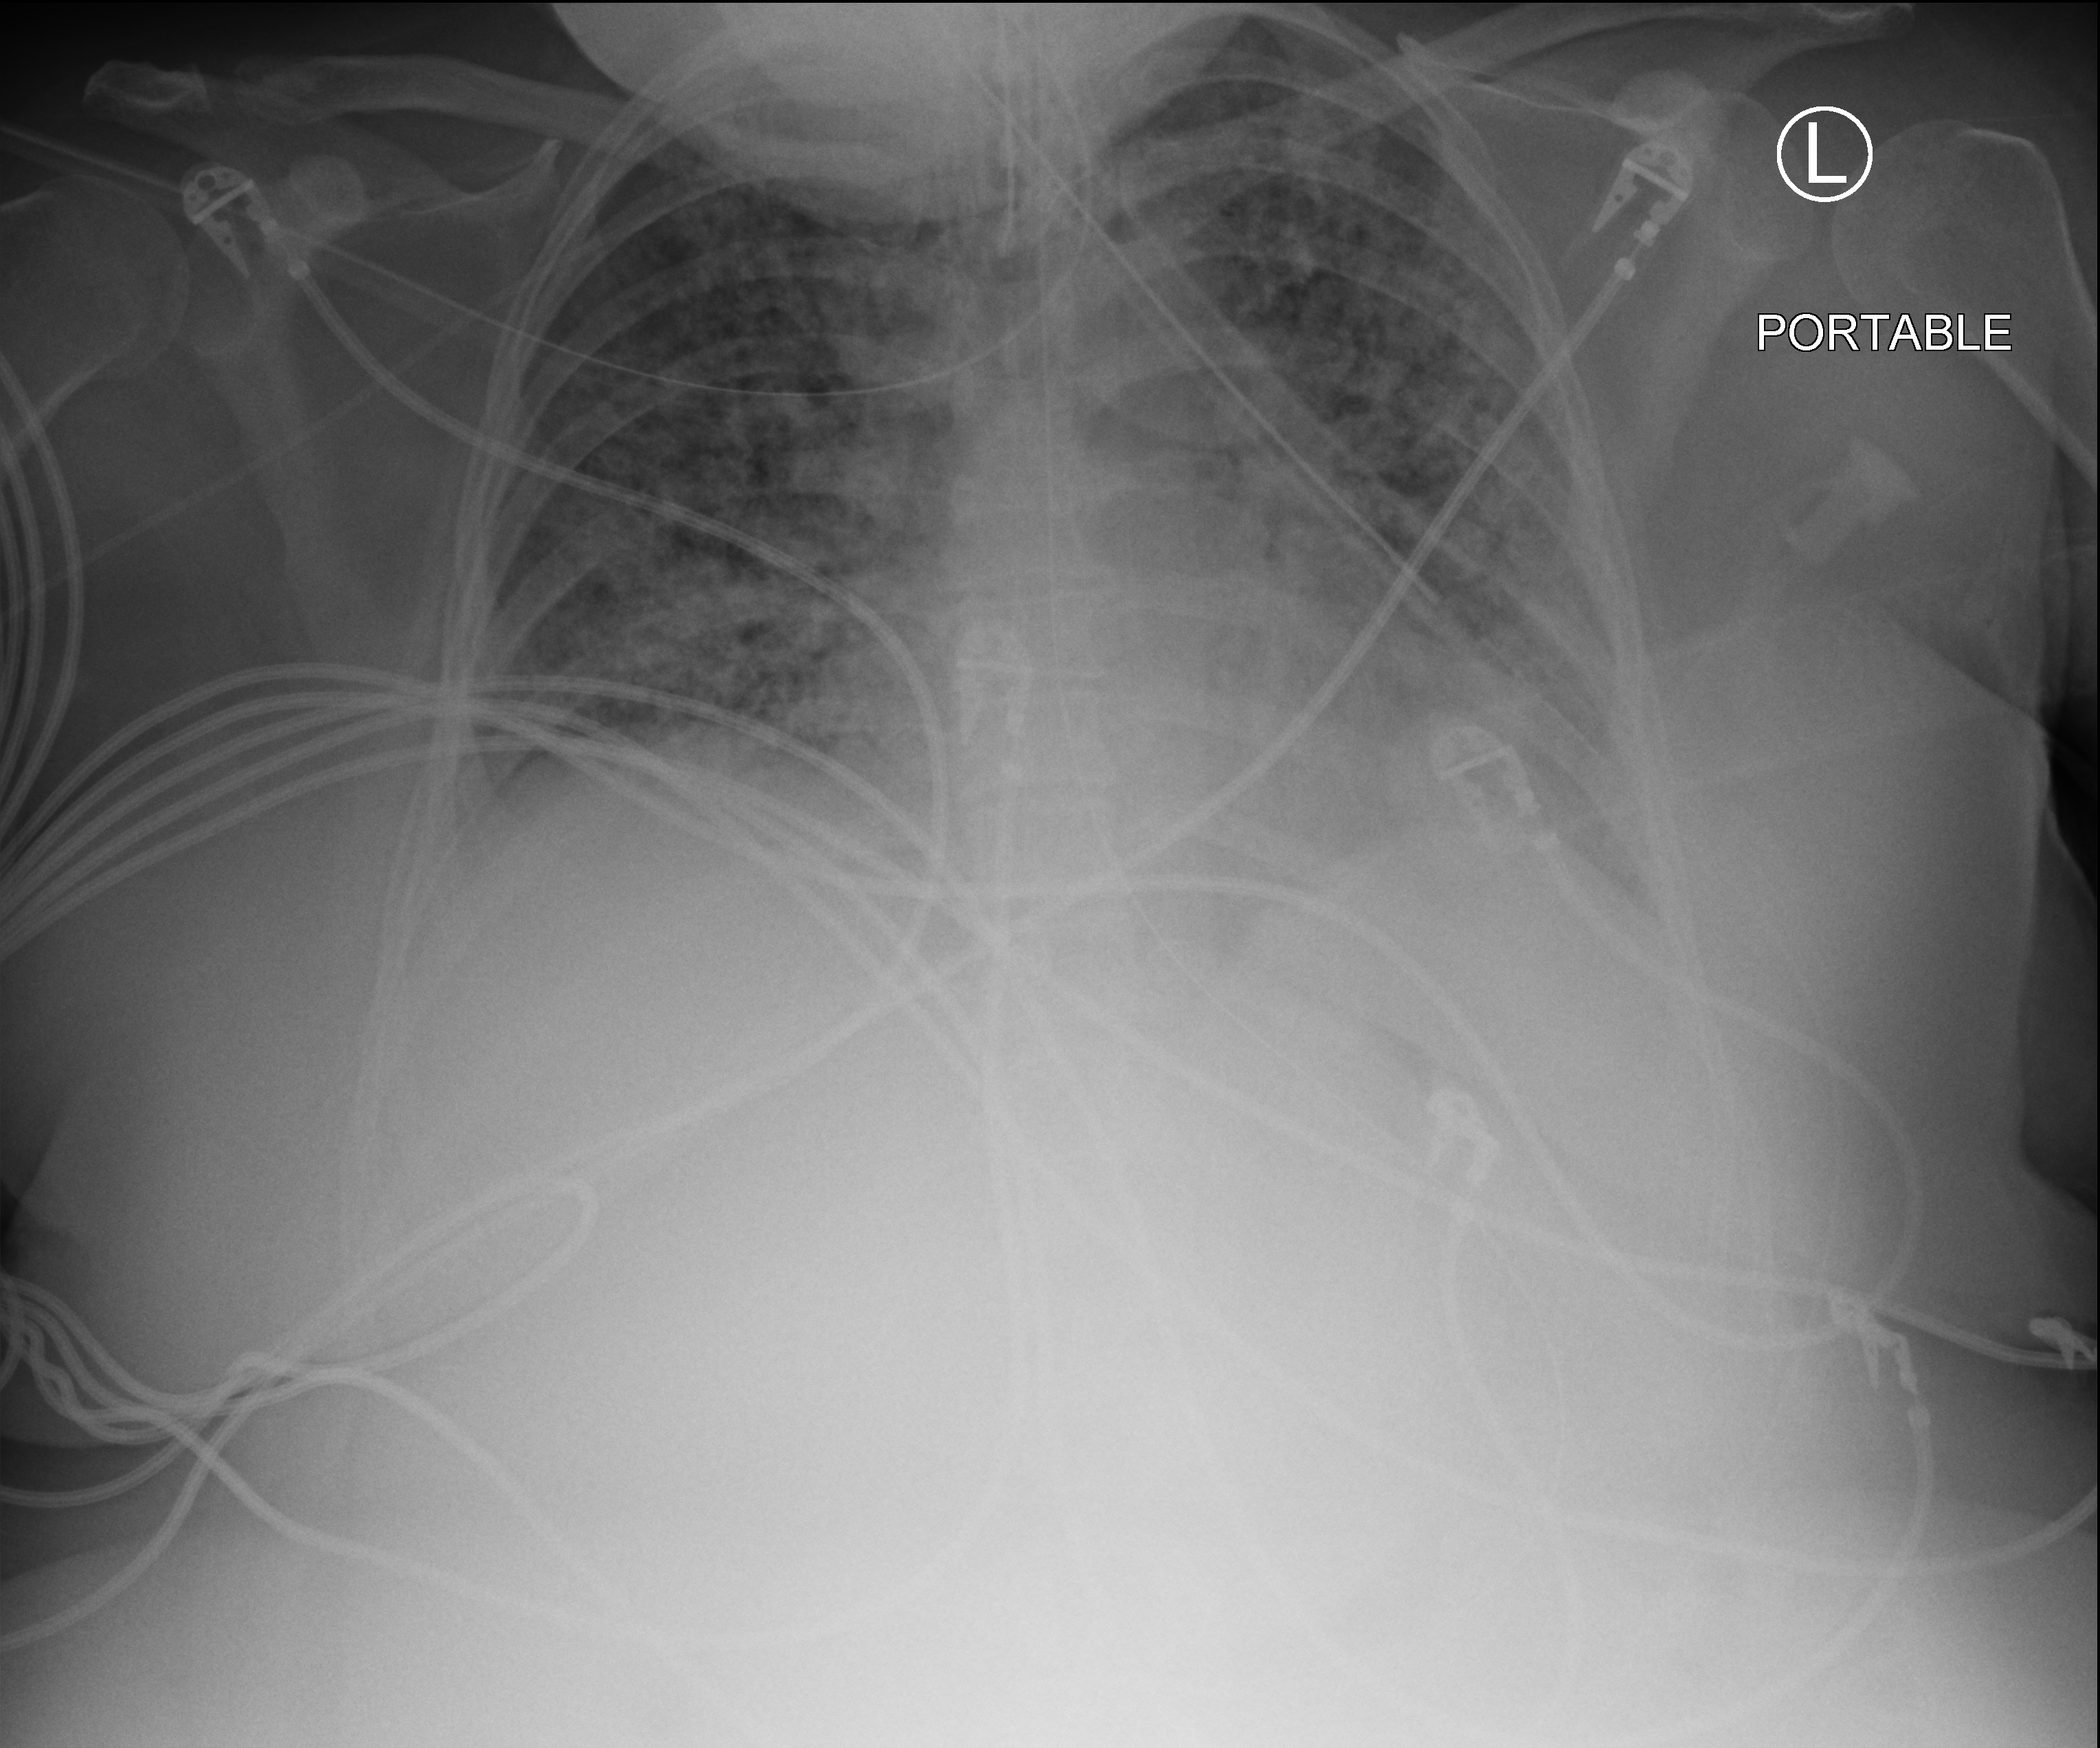
Bedside chest radiograph (computed radiography); anteroposterior (AP) projection. Patient hospitalised with COVID-19; female, aged 18–59 years.
Admission-level facts for this patient (not findings on this image; timing relative to this image not recorded): admitted to intensive care during this hospital stay: yes; hypertension (admission record): yes.